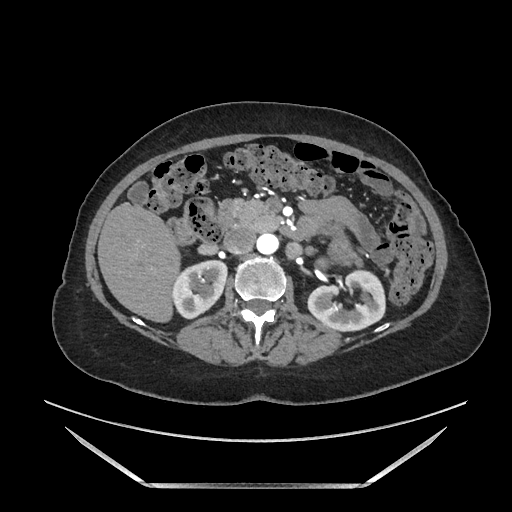
Contrast-enhanced abdominal CT, one axial slice. Soft-tissue window (W 400 / L 40 HU). 1.25 mm slice thickness. 512 × 512 image matrix, field of view 440 × 440 mm. Female patient. From the clinical record (not read from this slice): diagnosis: adrenocortical carcinoma; tumour side: left adrenal; tumour size at pathology: 12.5 cm; Ki-67 index: 39 %; stage (as recorded): 3.
Outlined on this slice (semi-automatic segmentation, software-assisted and operator-edited):
- mass: bounding box [x1, y1, x2, y2] px = [325, 223, 364, 268]